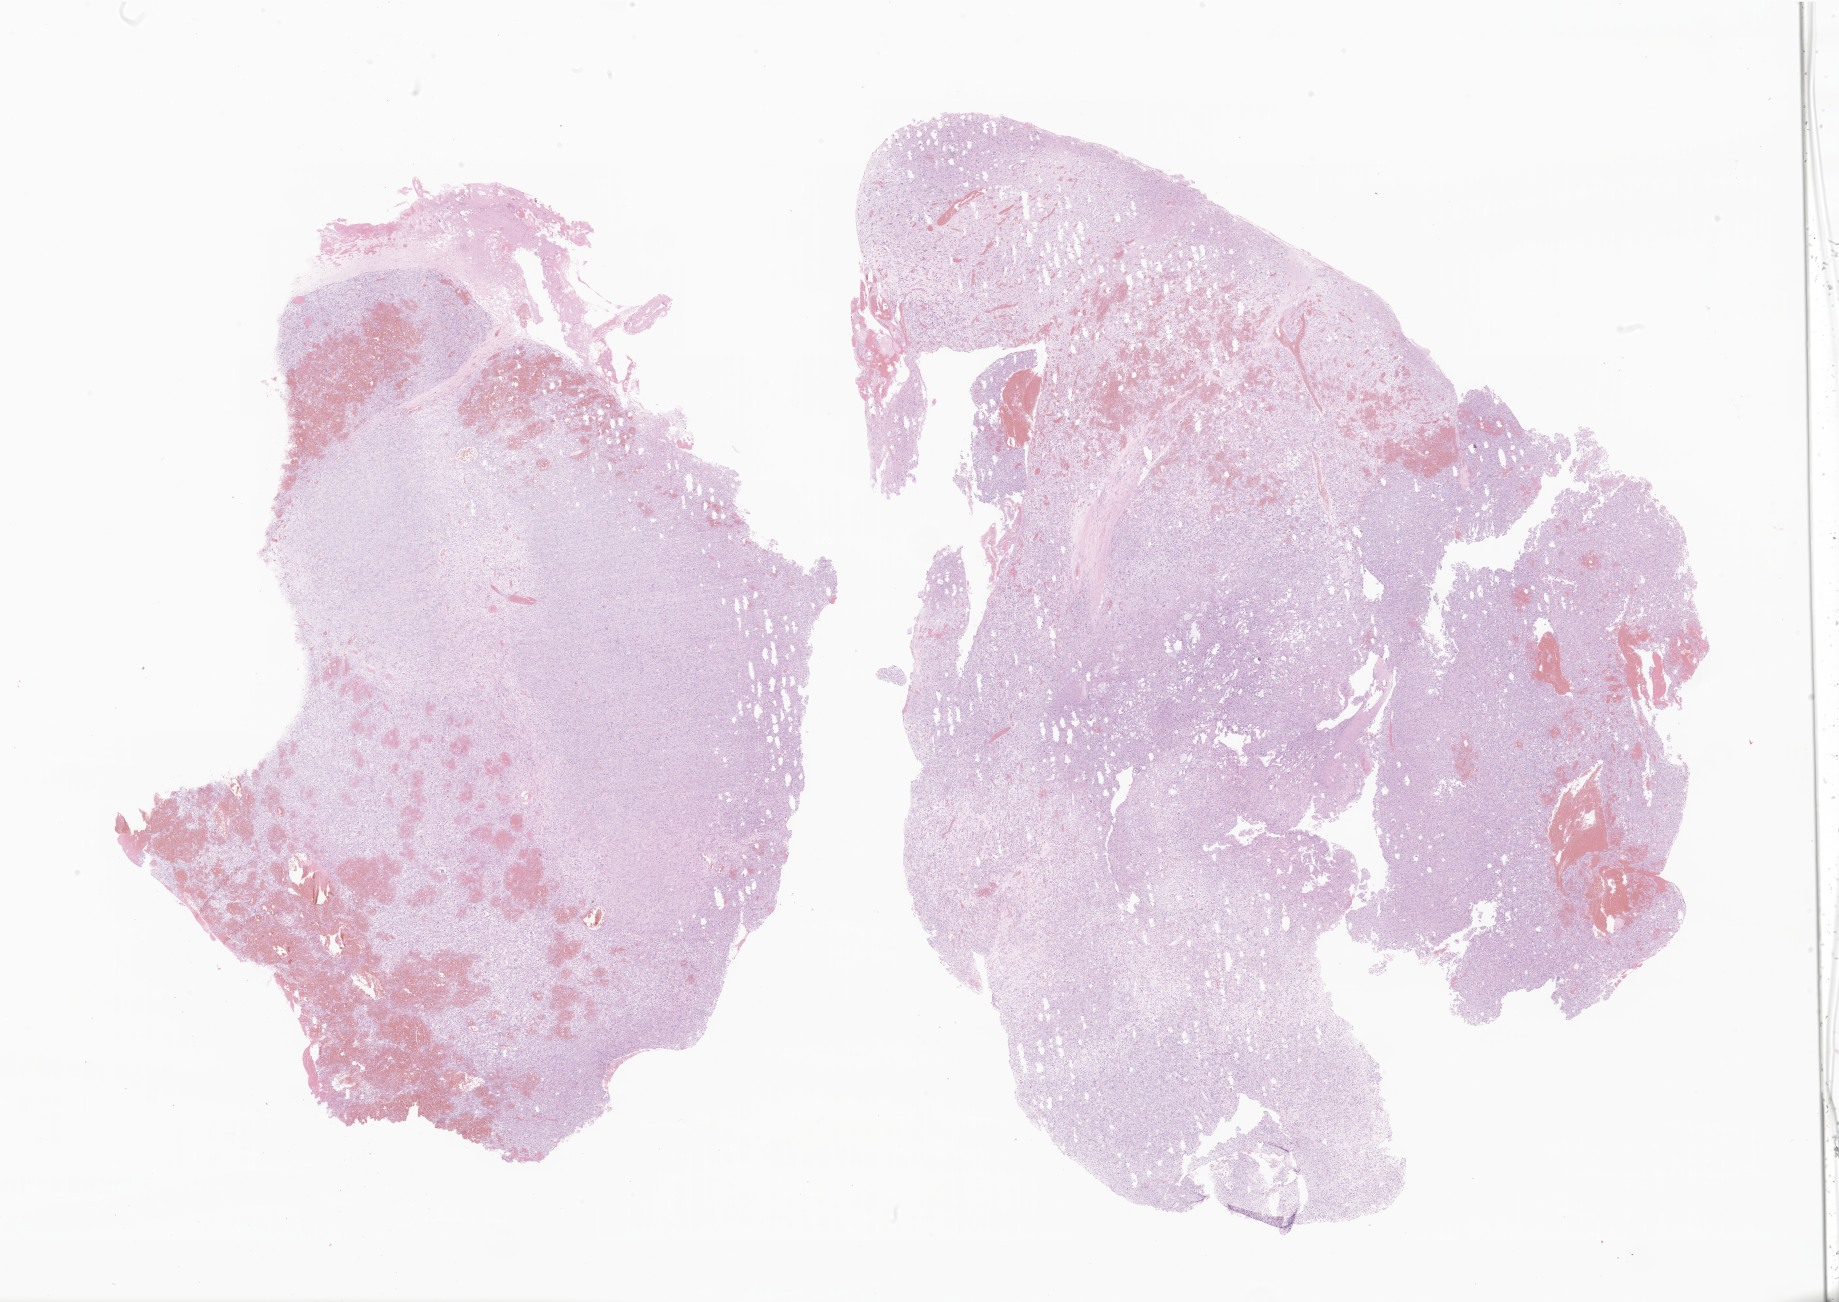
Whole-slide image, haematoxylin and eosin stain of tumor tissue from the brain — shown as a low-resolution overview of the whole scanned area (about 31.0 x 22.0 mm); formalin-fixed, paraffin-embedded (FFPE) tissue. Patient male; age 93 months (7 years 9 months).
Diagnosis (ICD-O-3 morphology term): Sarcoma, NOS.